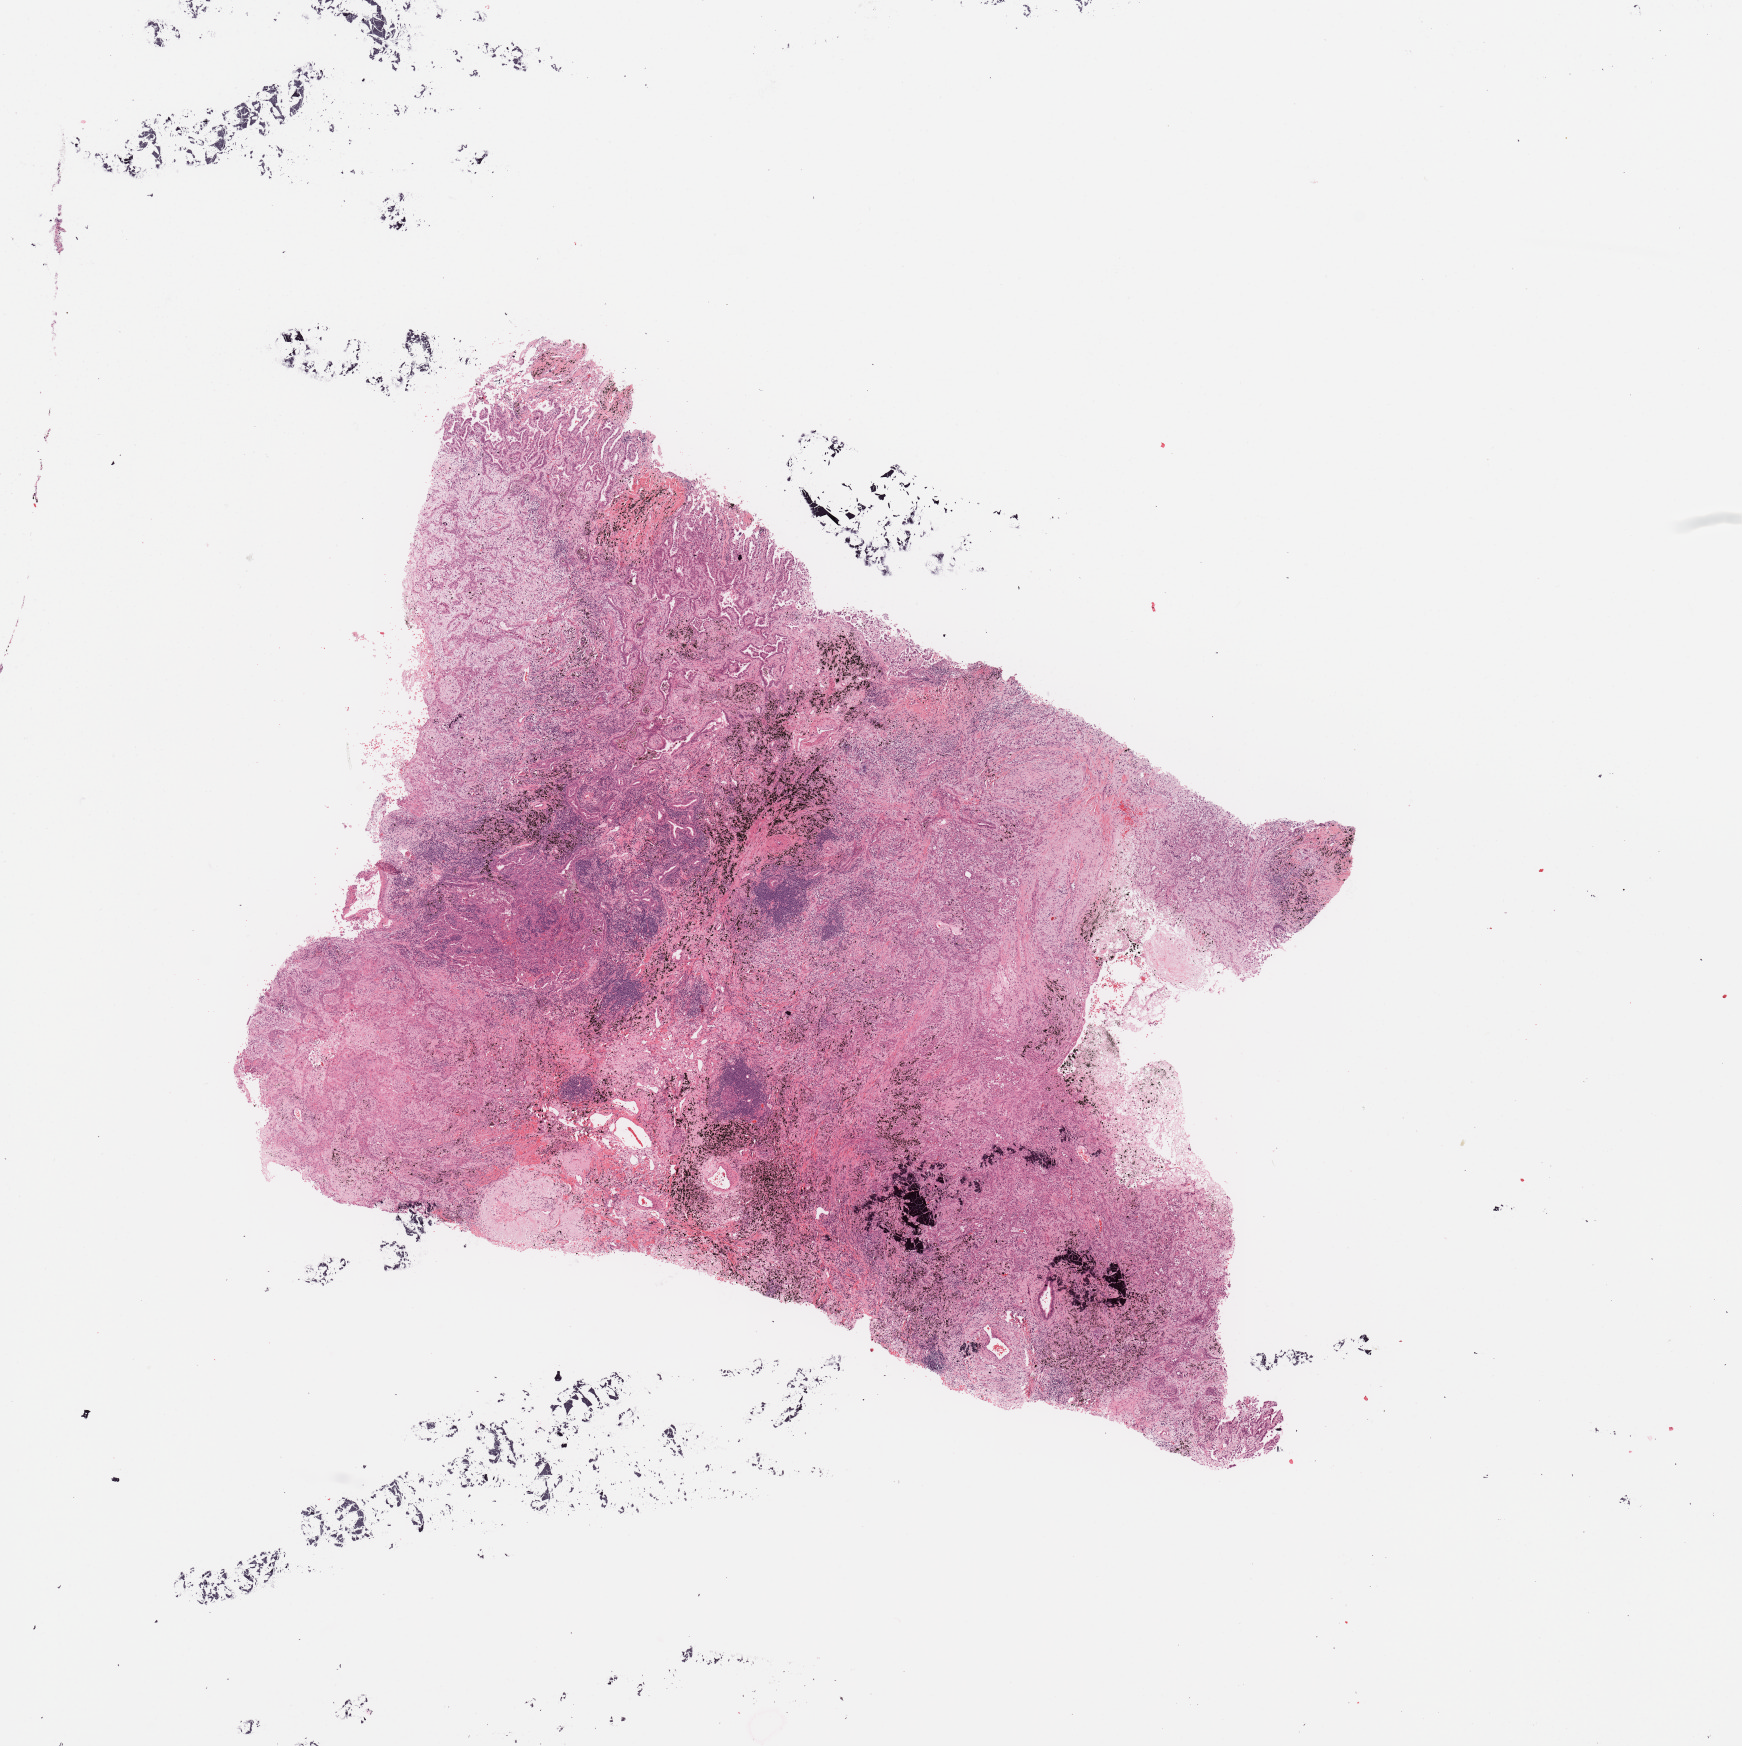
Whole-slide histology image, H&E-stained — whole scanned area (about 13.8 x 13.8 mm) shown as a low-resolution overview. Tumour tissue sample, sampled site: lung. Female, 69 y/o. Histologic grade: G3 (poorly differentiated). Slide review estimates, as recorded: tumour nuclei 60%, necrosis 7%.
• histologic diagnosis: Squamous cell carcinoma, NOS
• AJCC pathologic stage: IA
• primary tumour site (as recorded): right lower lobe